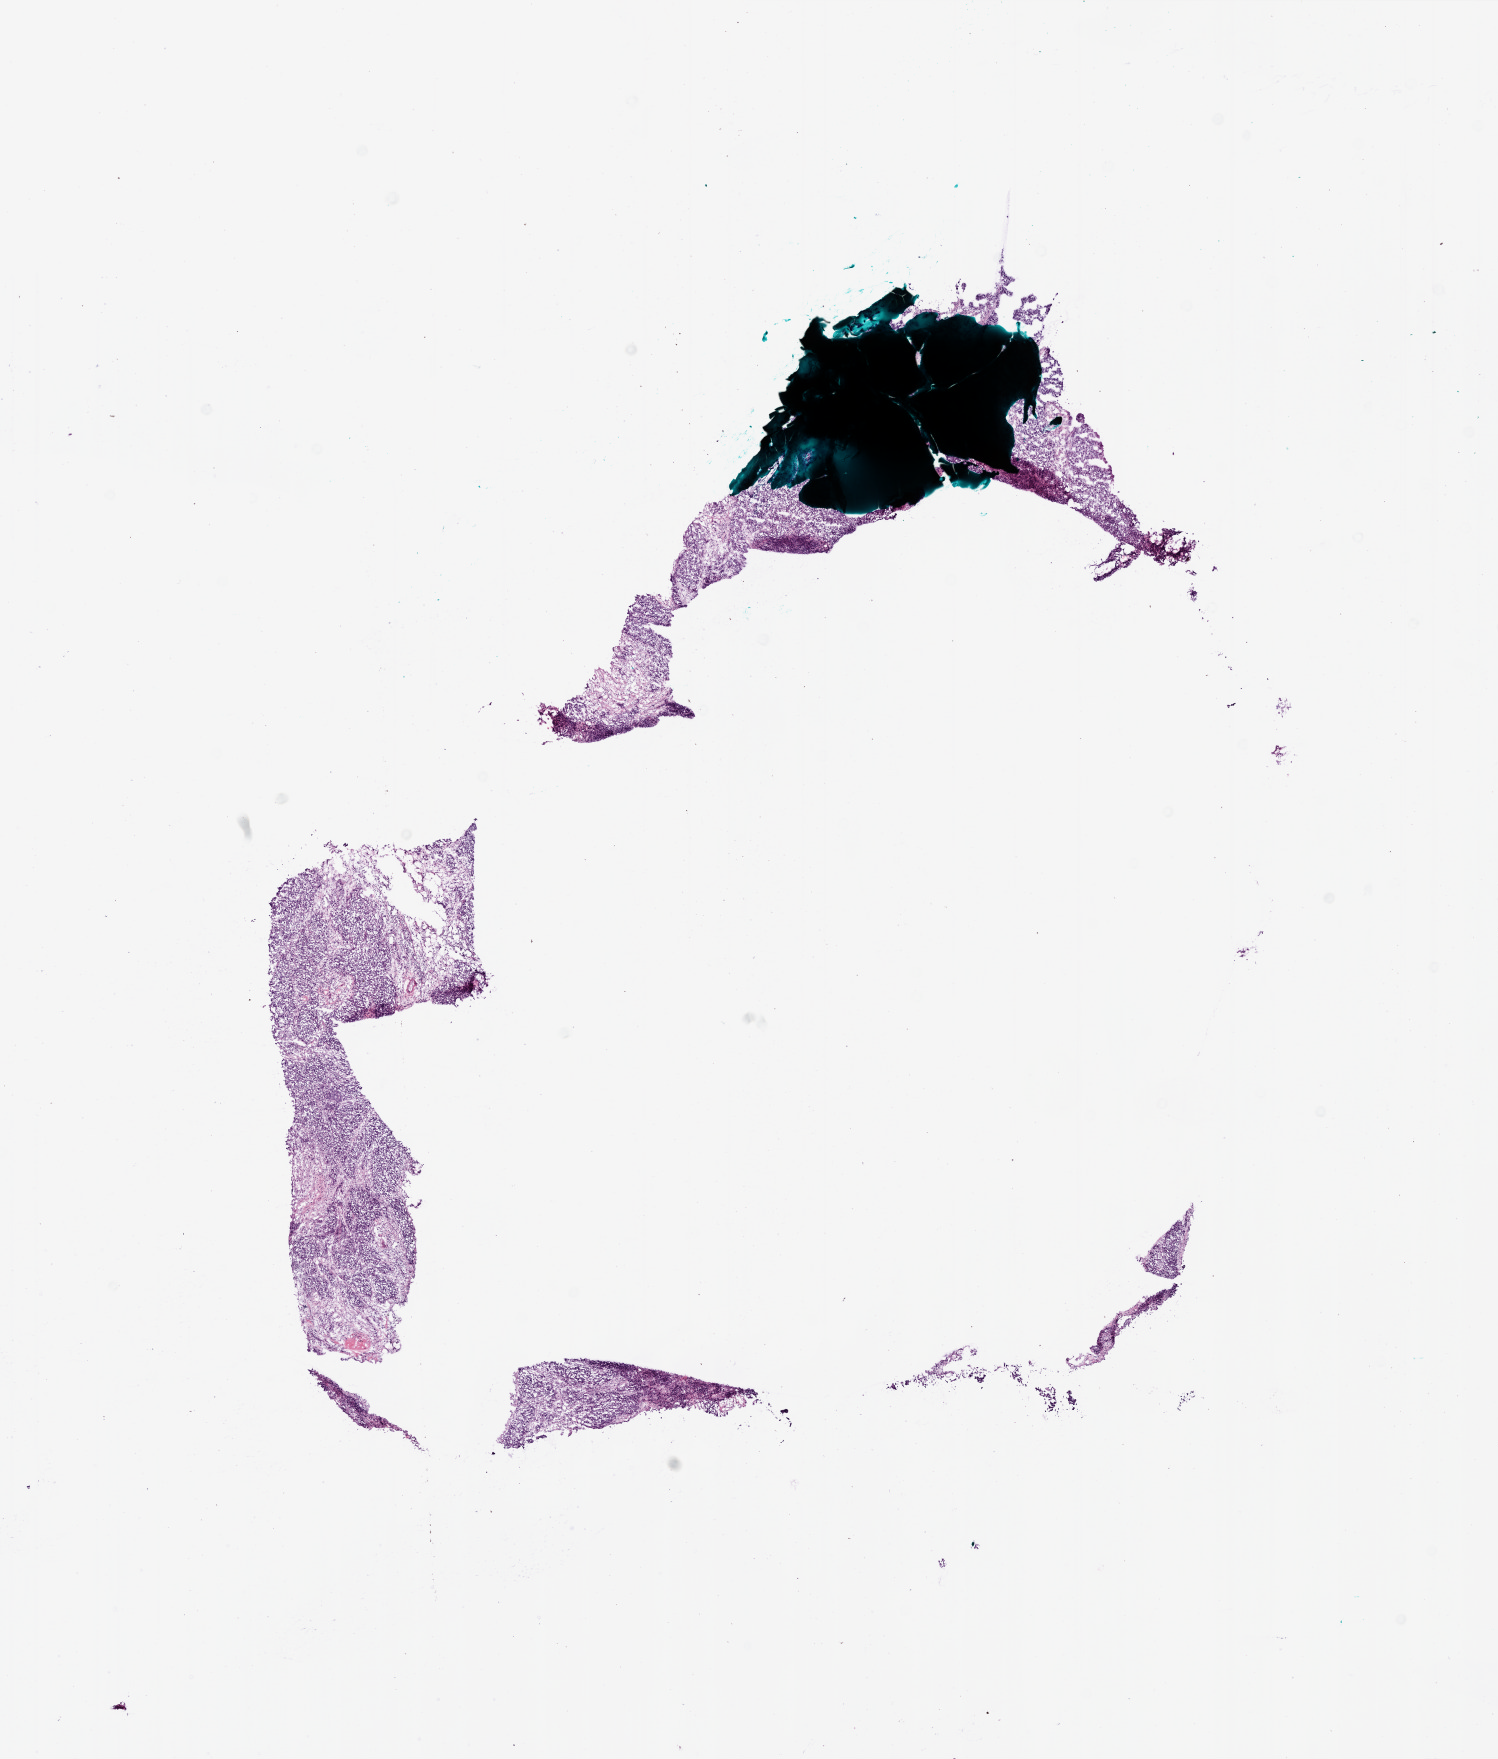
Digitized Hematoxylin and eosin (H&E) stained tissue section (whole slide), shown as a low-resolution overview of the whole scanned area (about 12.0 x 14.1 mm), frozen section, sample: primary tumour, ovary. Female, age 70 years at initial diagnosis. Histologic grade: G3 (poorly differentiated). Composition of this section per pathologist review: tumour cells 78%, tumour nuclei 80%, normal cells 20%, stromal cells 0%, necrosis 2%.
FIGO stage: IIIC. Laterality: left. Histologic diagnosis: Serous cystadenocarcinoma, NOS.